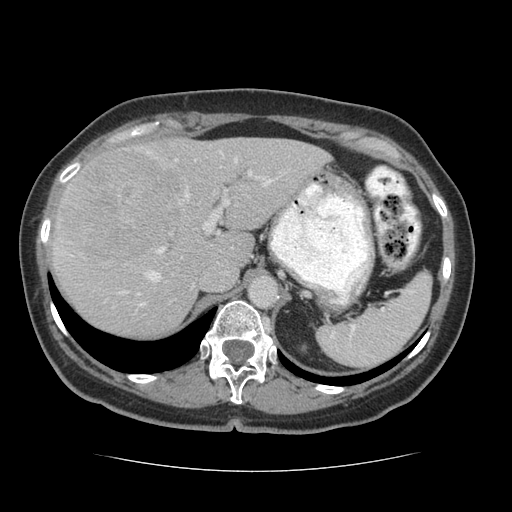
Contrast-enhanced abdominal CT (liver protocol), one axial slice. Slice 45 of 75 in the series (ordered by position). 140 kVp. Soft-tissue window (W 400 / L 40 HU). 512 × 512 image matrix, field of view 360 × 360 mm. Case-level facts recorded for this patient, not image findings: diagnosis: hepatocellular carcinoma (patient treated with transarterial chemoembolisation; whether this scan precedes or follows treatment is not stated here); TNM stage (as recorded): Stage-I; Child-Pugh class: A; tumour differentiation: moderately differentiated; tumour nodularity: uninodular.
Structures marked on this image (semi-automatic segmentation, software-assisted and operator-edited):
- liver parenchyma outside the tumour (the mass and vessels are separate outlines, so this box may not span the whole liver): bounding box <52,138,330,336> (left, top, right, bottom; pixels)
- mass: <57,148,190,263>
- liver vessels: <55,151,272,306>